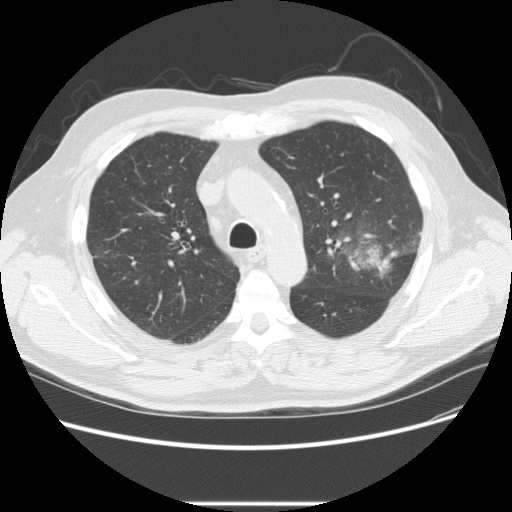
Chest CT (low-dose screening protocol), one axial image; baseline annual screen; lung window (W 1500 / L -600 HU); slice 71 of 233 in the series. Male participant, aged 73 years at enrolment. Former smoker at enrolment.
Expert reader's lesion annotation, box from (x=332, y=215) to (x=420, y=288) px. The screening reader recorded 2 non-calcified nodules or masses ≥4 mm on this exam; which of them this box marks is not recorded.